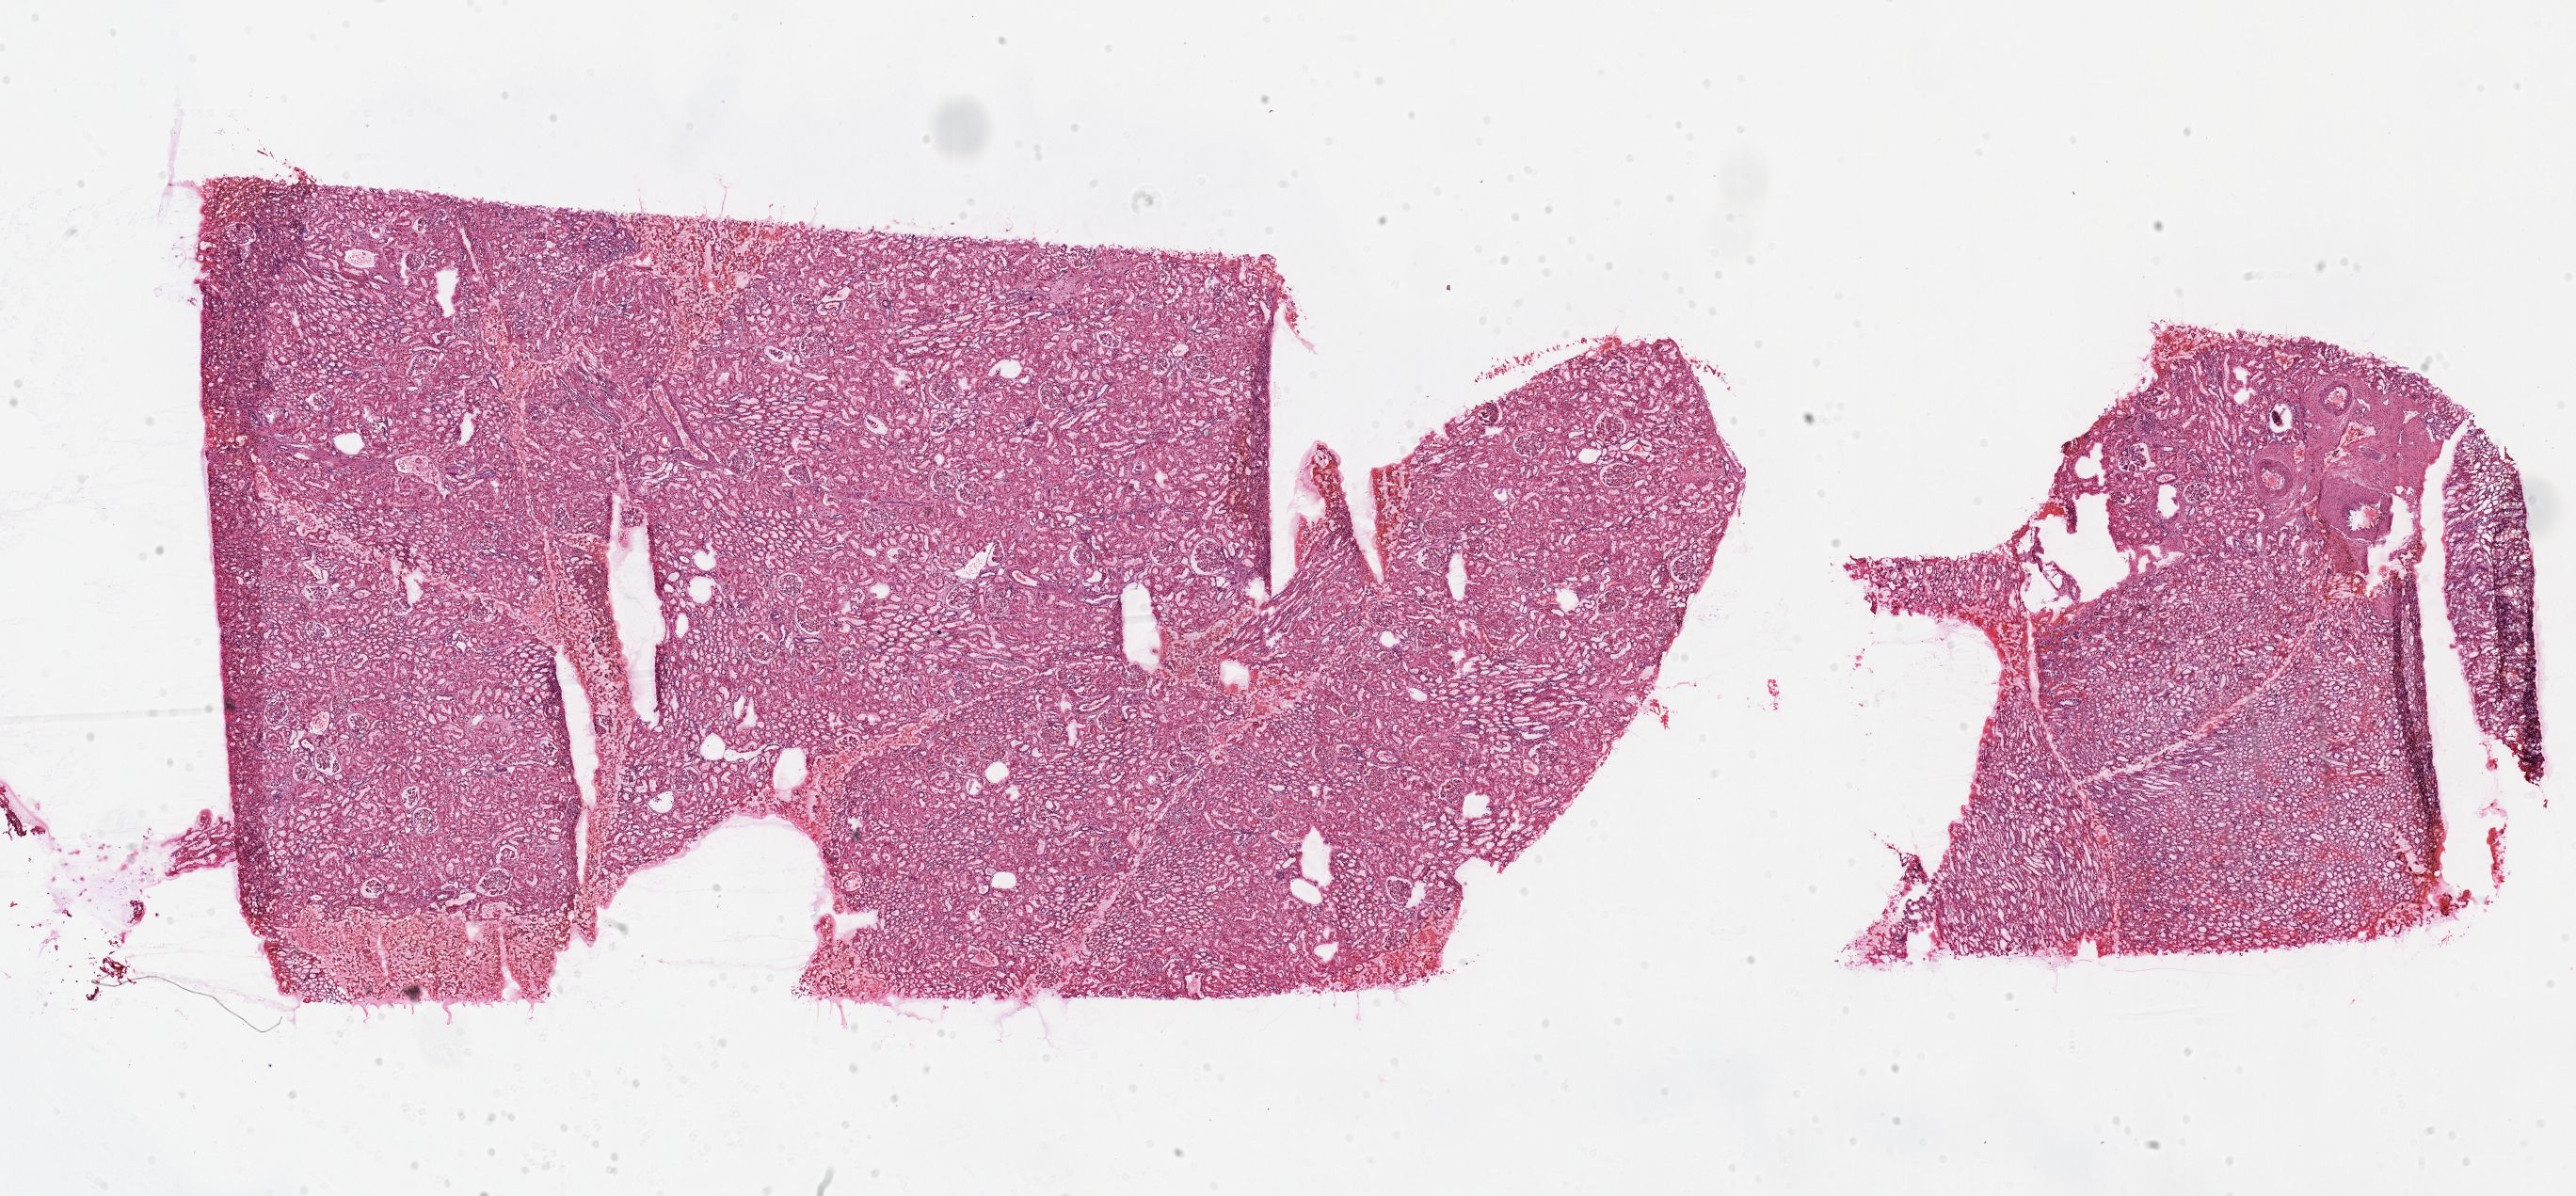
H&E whole-slide image, low-resolution overview of the scanned area, about 21.7 x 10.1 mm (slide scanned at 20x), frozen section from the top of the tissue portion, solid tissue normal (non-tumour tissue) sample from the kidney. Male, age 51 years at initial diagnosis.
* this section: solid tissue normal (non-tumour) sample from the same patient
* patient diagnosis: Clear cell adenocarcinoma, NOS